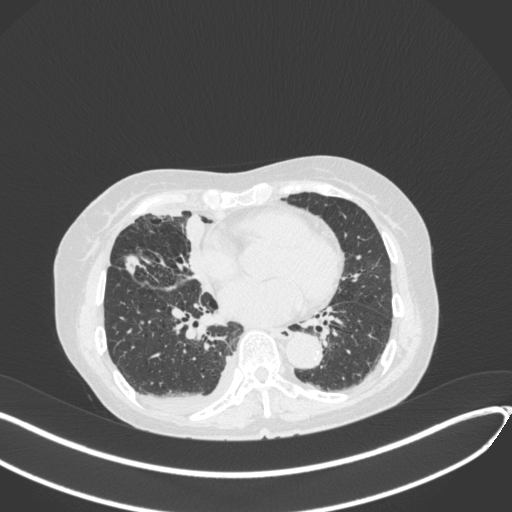
Chest CT, one axial slice; slice 166 of 418 in the series (ordered by position); lung window (W 1500 / L -600 HU); 1 mm slice thickness; 512 × 512 image matrix, field of view 400 × 400 mm. Female patient, age 75 years. Case-level facts recorded for this patient, not image findings: clinical TNM (as recorded): T2a N3 M0.
Structures marked on this image (bounding box drawn by a radiologist):
- lung tumour (recorded histology: adenocarcinoma): bounding box <122,250,146,275> (left, top, right, bottom; pixels)